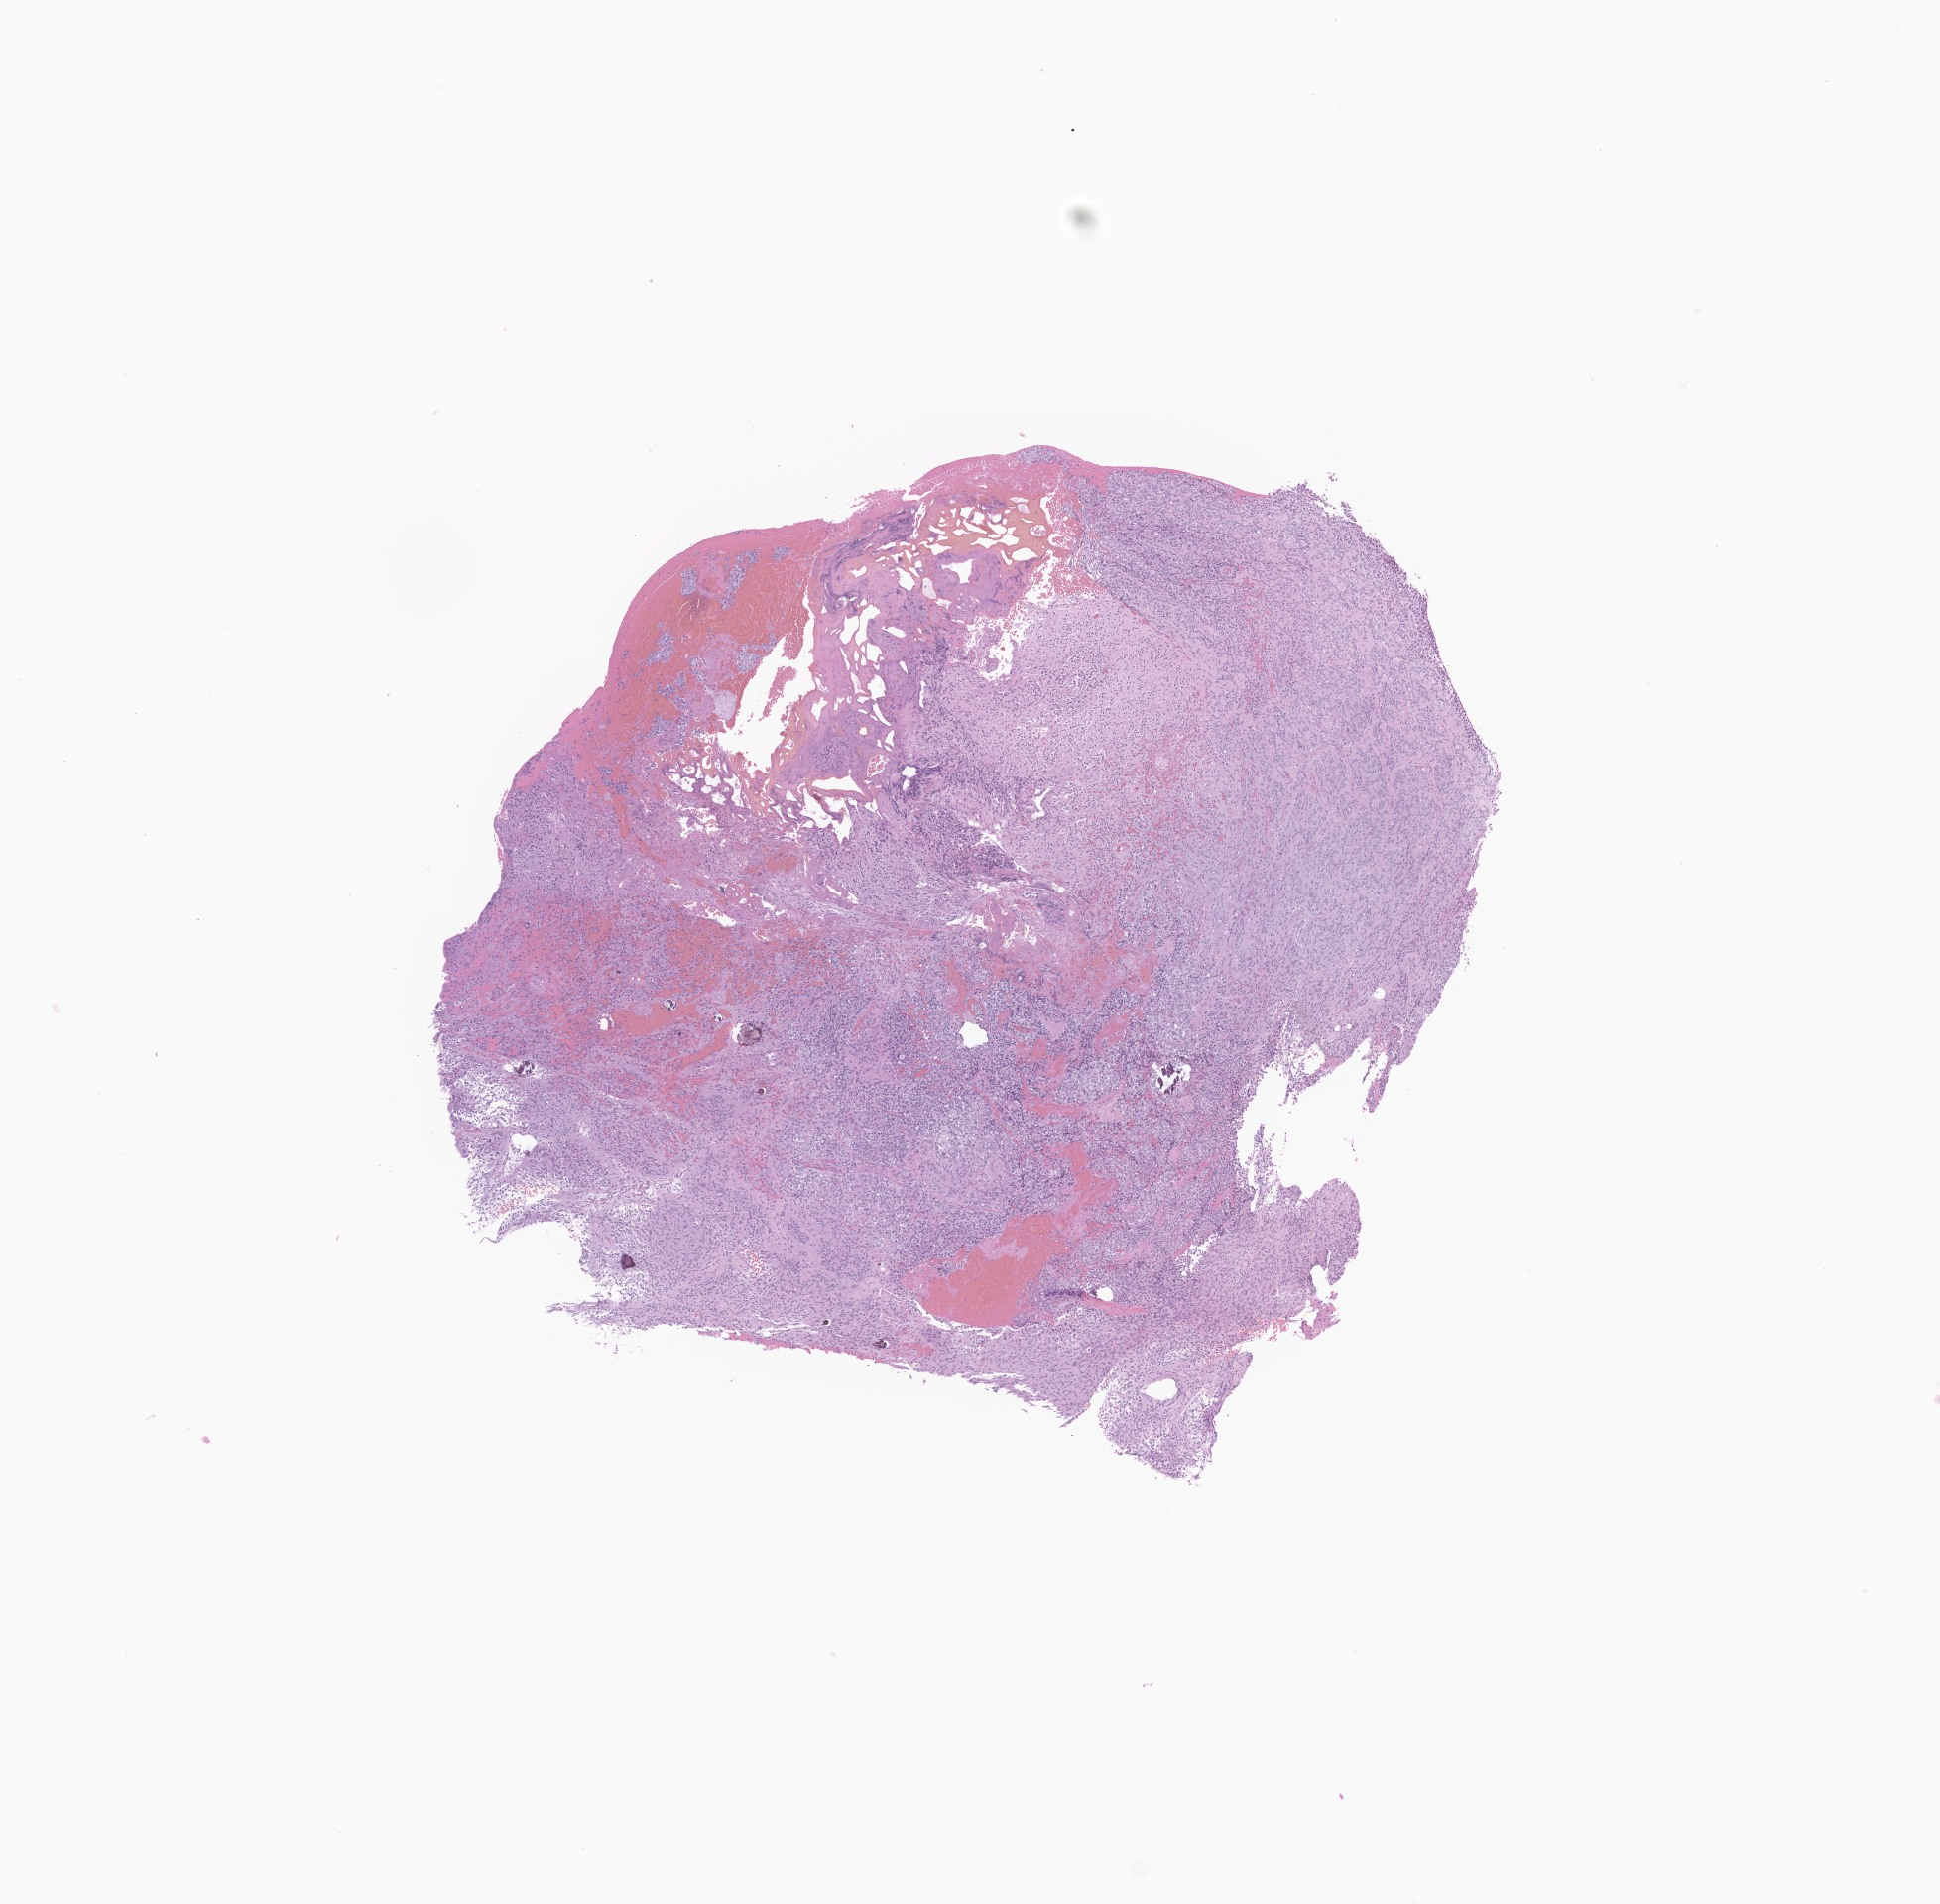
Haematoxylin and eosin whole-slide image of tumor tissue from the pineal gland — a low-resolution overview of the entire scanned area, about 8.2 x 8.1 mm. Formalin-fixed paraffin-embedded section. Patient female; age 225 months (18 years 9 months).
- recorded diagnosis: Pinealoma